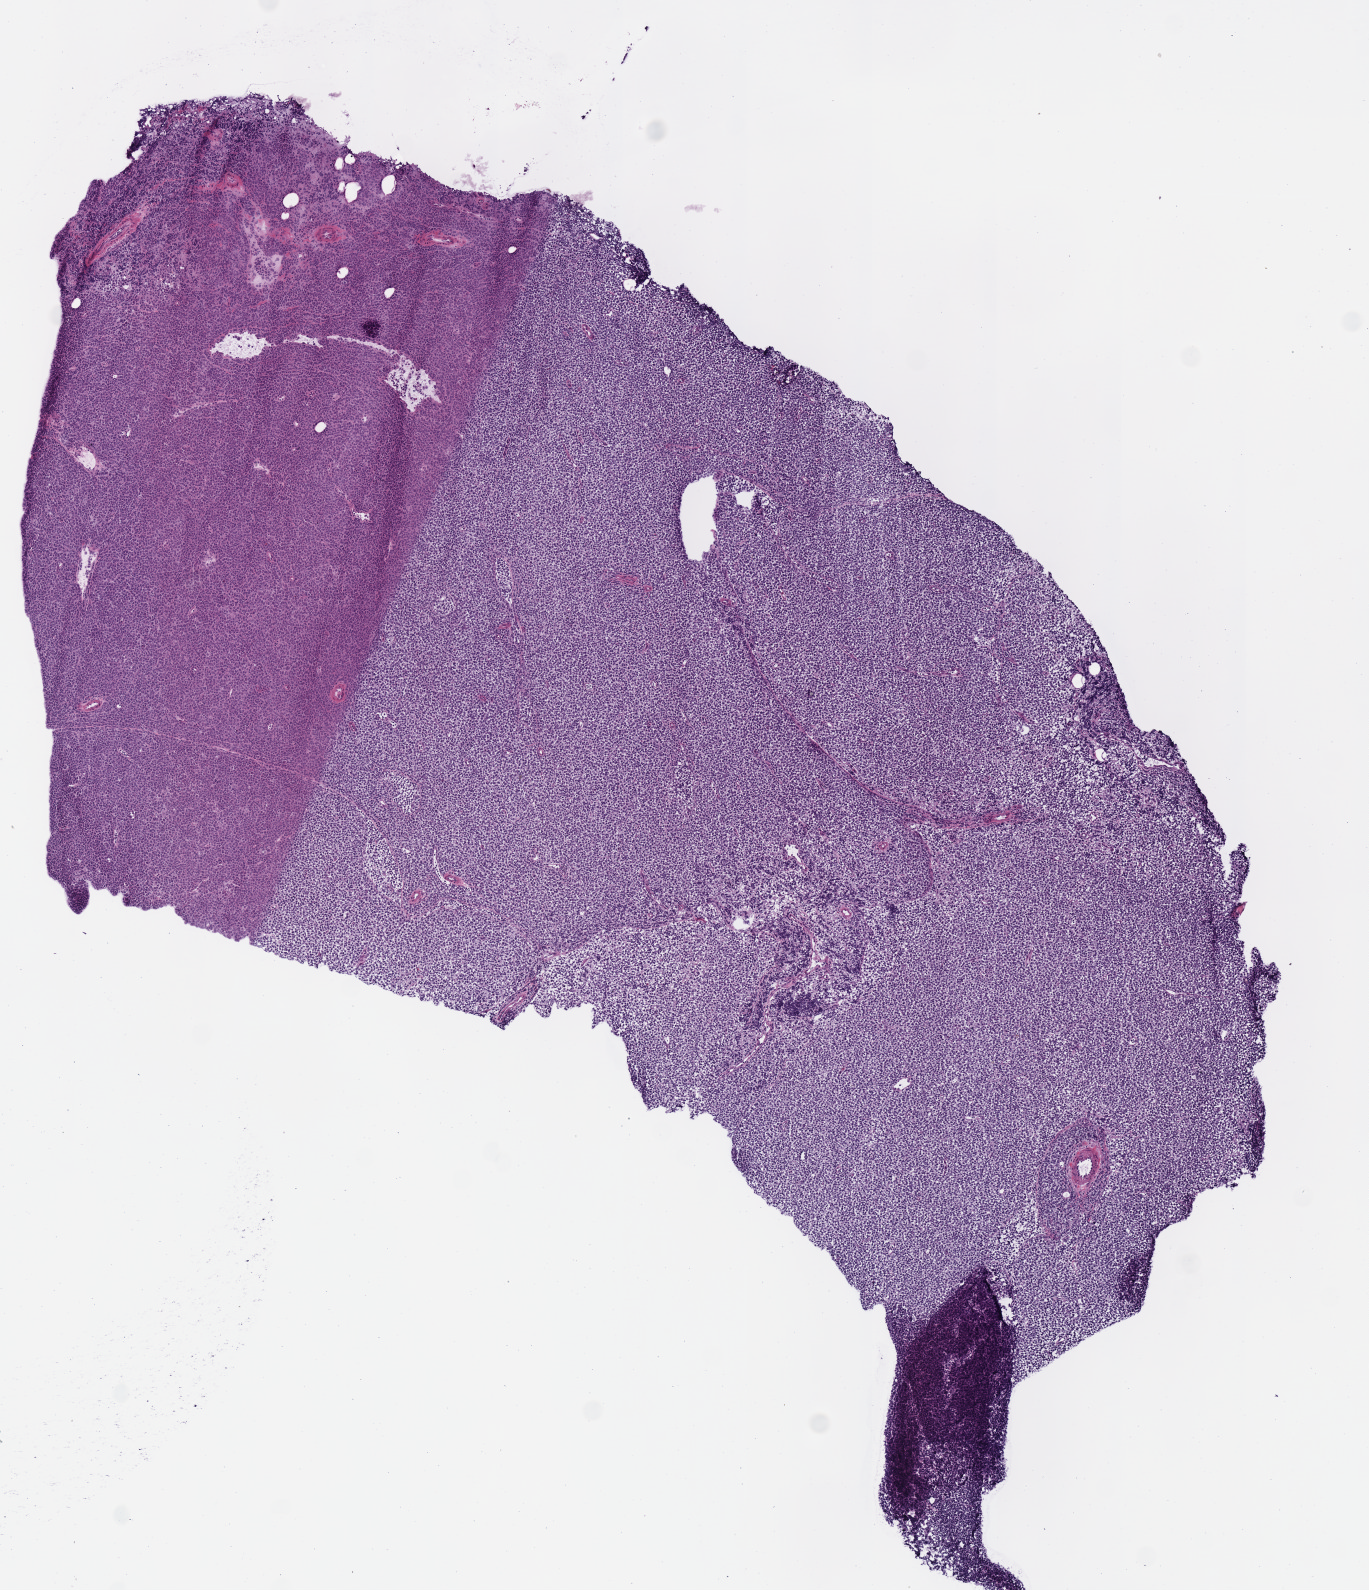
Whole-slide histology image, H&E-stained, shown as a low-resolution overview of the whole scanned area (about 5.4 x 6.3 mm, slide scanned at 40x). Frozen section. Lymphoid tissue, primary tumour sample. Female, age 38 years at initial diagnosis. Composition of this section per pathologist review: tumour cells 100%, tumour nuclei 95%, normal cells 0%, stromal cells 0%, necrosis 0%. Infiltration values recorded for this section: lymphocyte infiltration 2%, monocyte infiltration 0%, neutrophil infiltration 0%.
Pathologic diagnosis: Diffuse large B-cell lymphoma, NOS (lymph nodes of head, face and neck).